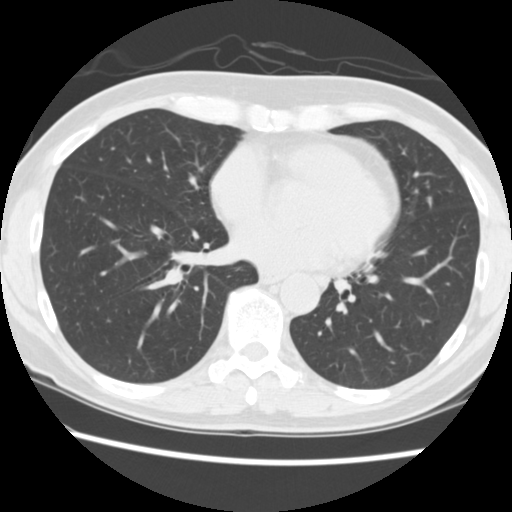
Axial slice from a low-dose chest CT screening exam; second annual screen; lung window (W 1500 / L -600 HU); 2.5 mm slice thickness; slice 147 of 258 in the series; 512 × 512 image matrix, field of view 330 × 330 mm. Female, age 60 years at enrolment. Current smoker at enrolment.
Expert-annotated lung lesion, box from (x=413, y=186) to (x=447, y=220) px. No non-calcified nodule or mass ≥4 mm was recorded by the screening reader at this exam. Official screen result: negative screen, minor abnormalities not suspicious for lung cancer. Participant outcome: lung cancer diagnosed 509 days after this screen (after the third annual screen) — adenocarcinoma, NOS, lingula, poorly differentiated (G3), stage IA (AJCC 6th edition), 6 mm at pathology.